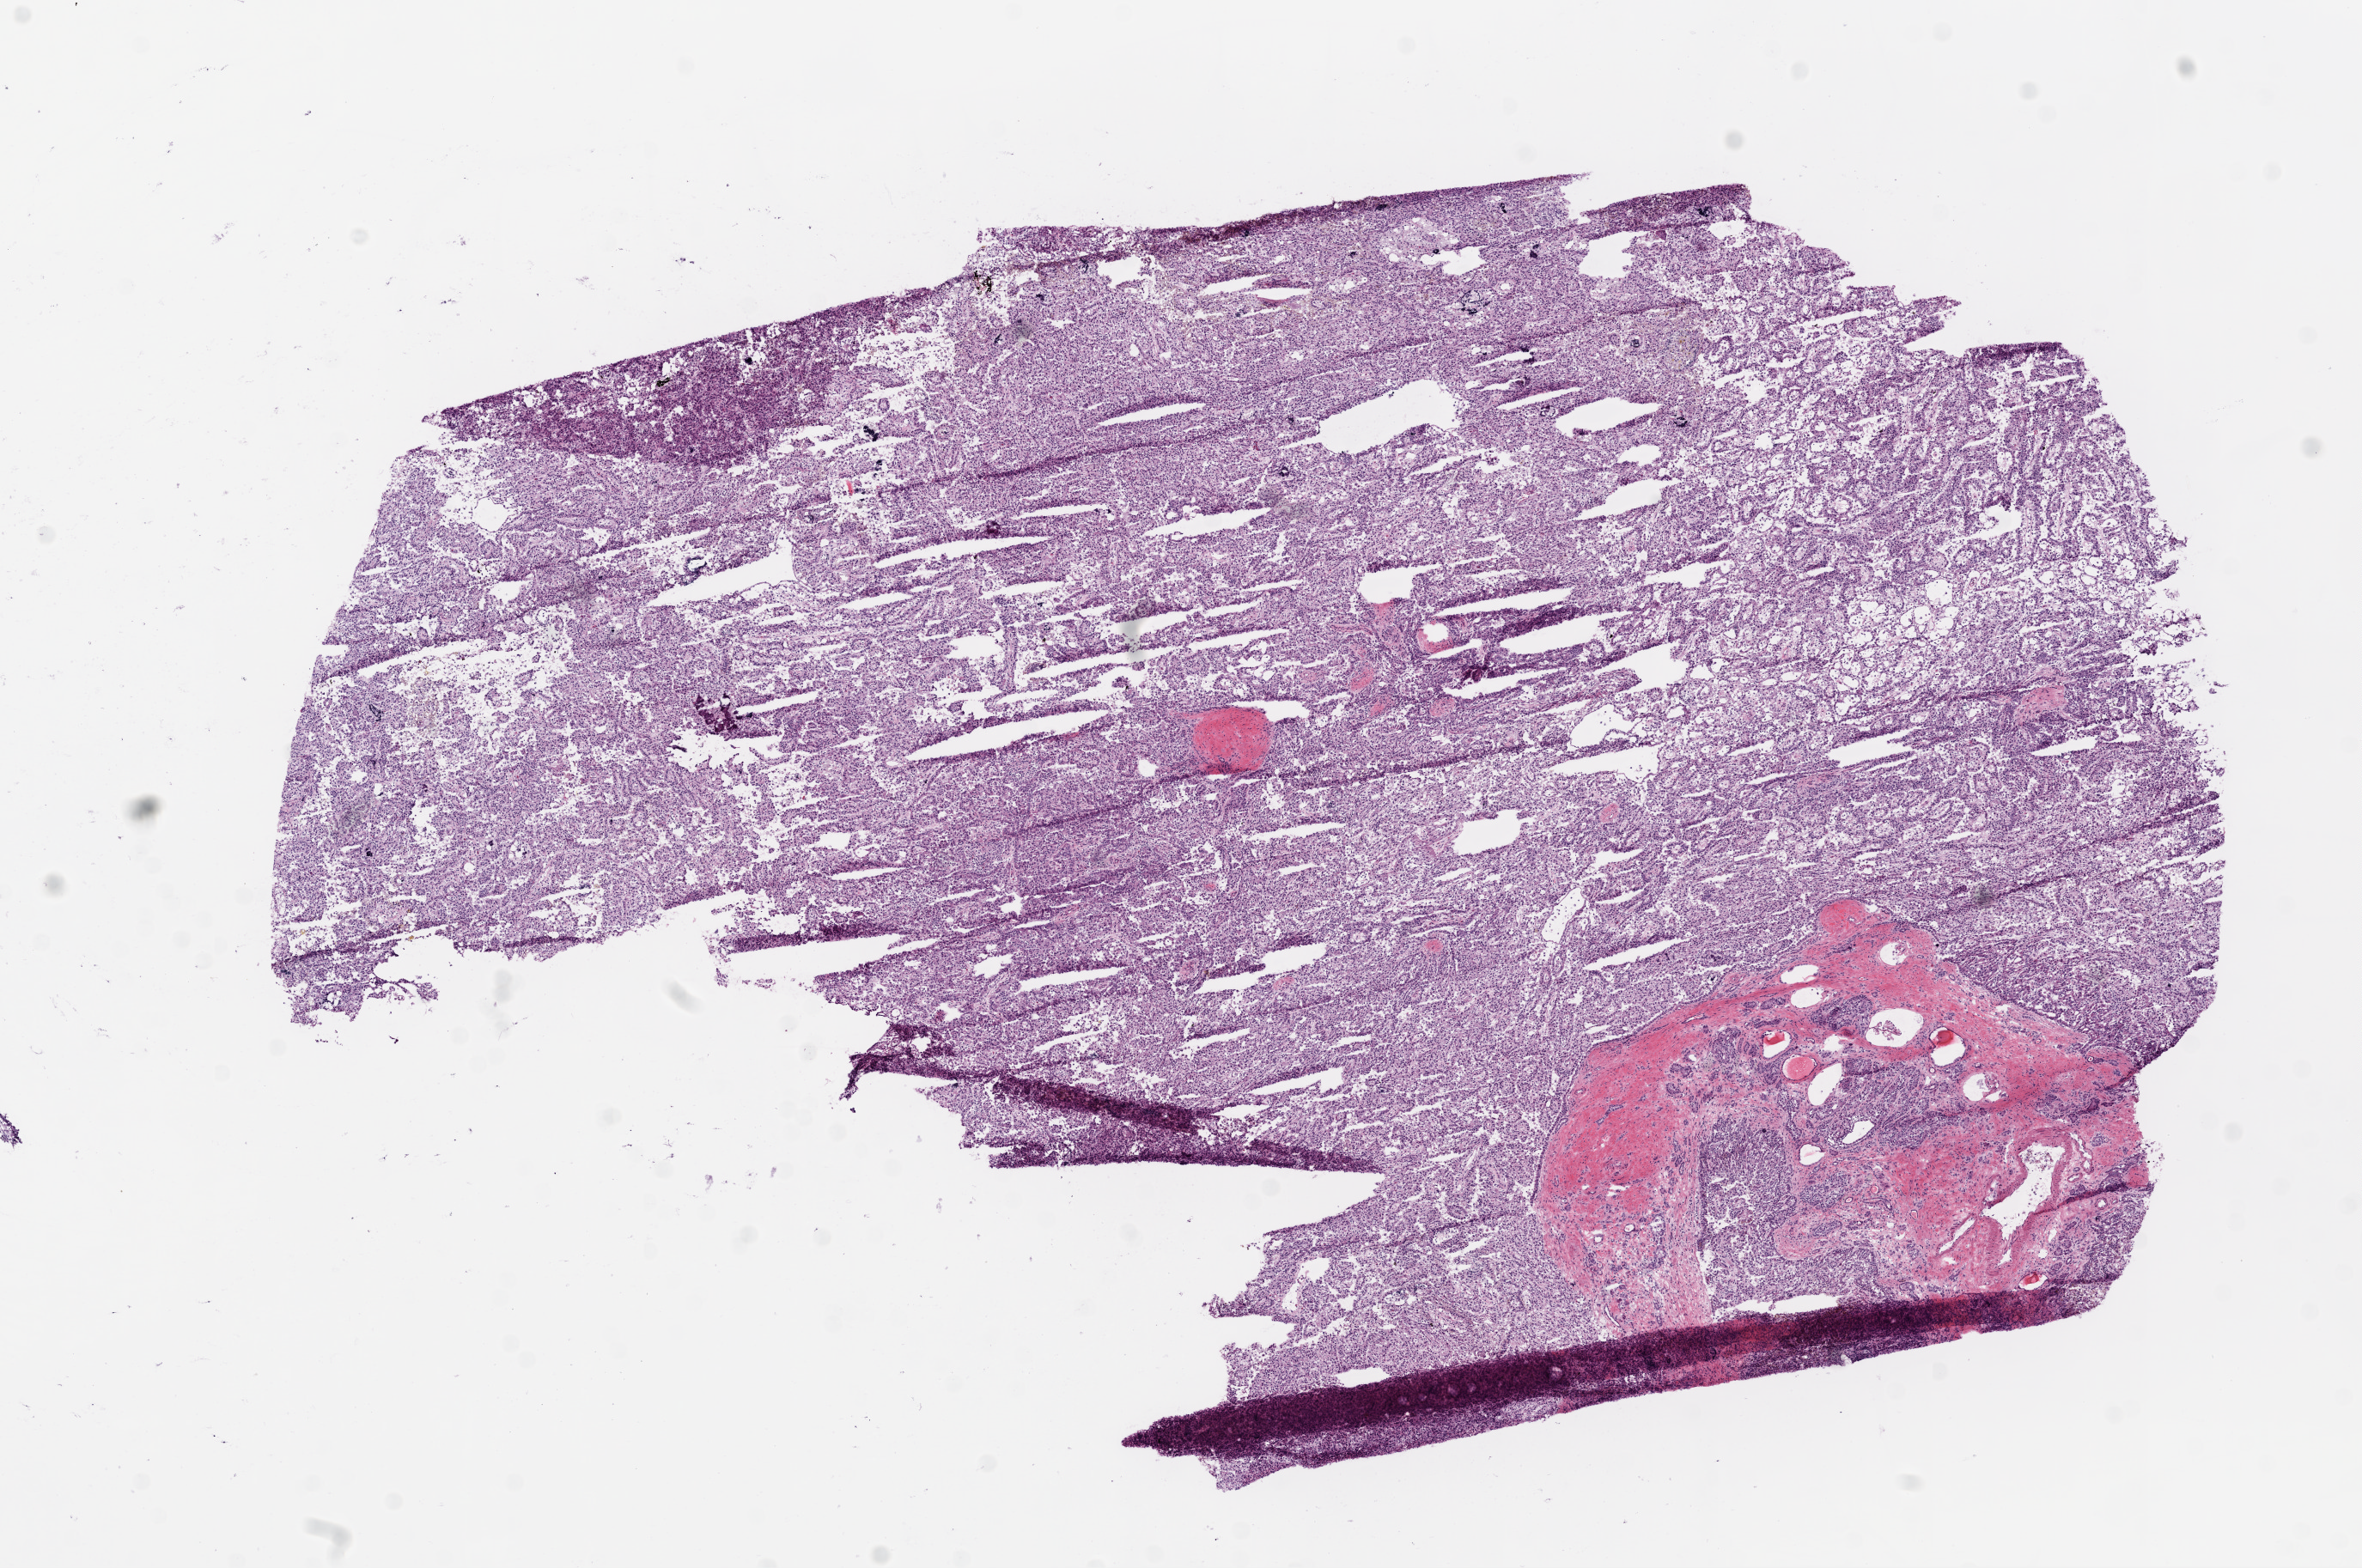
H&E-stained whole-slide image, low-resolution overview of the scanned area, about 11.0 x 7.3 mm (from a 20x scan). Frozen section. Primary tumour sample from the kidney. Patient: male, age at initial diagnosis 52 years. Composition of this section per pathologist review: tumour cells 92%, tumour nuclei 85%, normal cells 0%, stromal cells 8%, necrosis 0%.
- TNM: T3a NX M0
- AJCC pathologic stage: III
- diagnosis: Papillary adenocarcinoma, NOS
- laterality: left